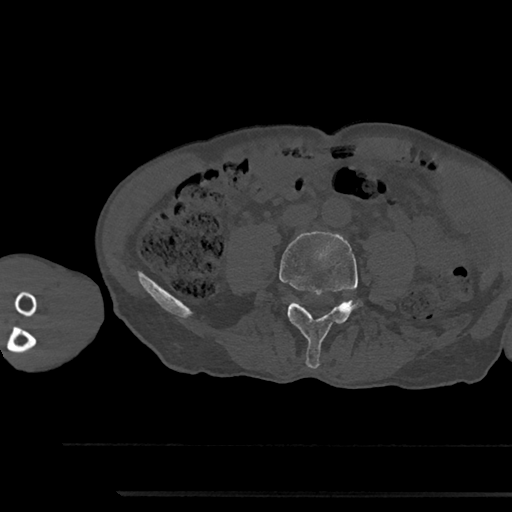
CT including the spine, one axial slice; slice 404 of 797 in the series (ordered by position); reconstruction kernel Br40s/3; 120 kVp; bone window (W 1800 / L 400 HU); 512 × 512 image matrix, field of view 367 × 367 mm. Patient: male, 79 years. Case-level facts recorded for this patient, not image findings: primary cancer: prostate.
Structures marked on this image (semi-automatically segmented with operator editing):
- L4 vertebra: bounding box [x1, y1, x2, y2] px = [279, 231, 358, 369]